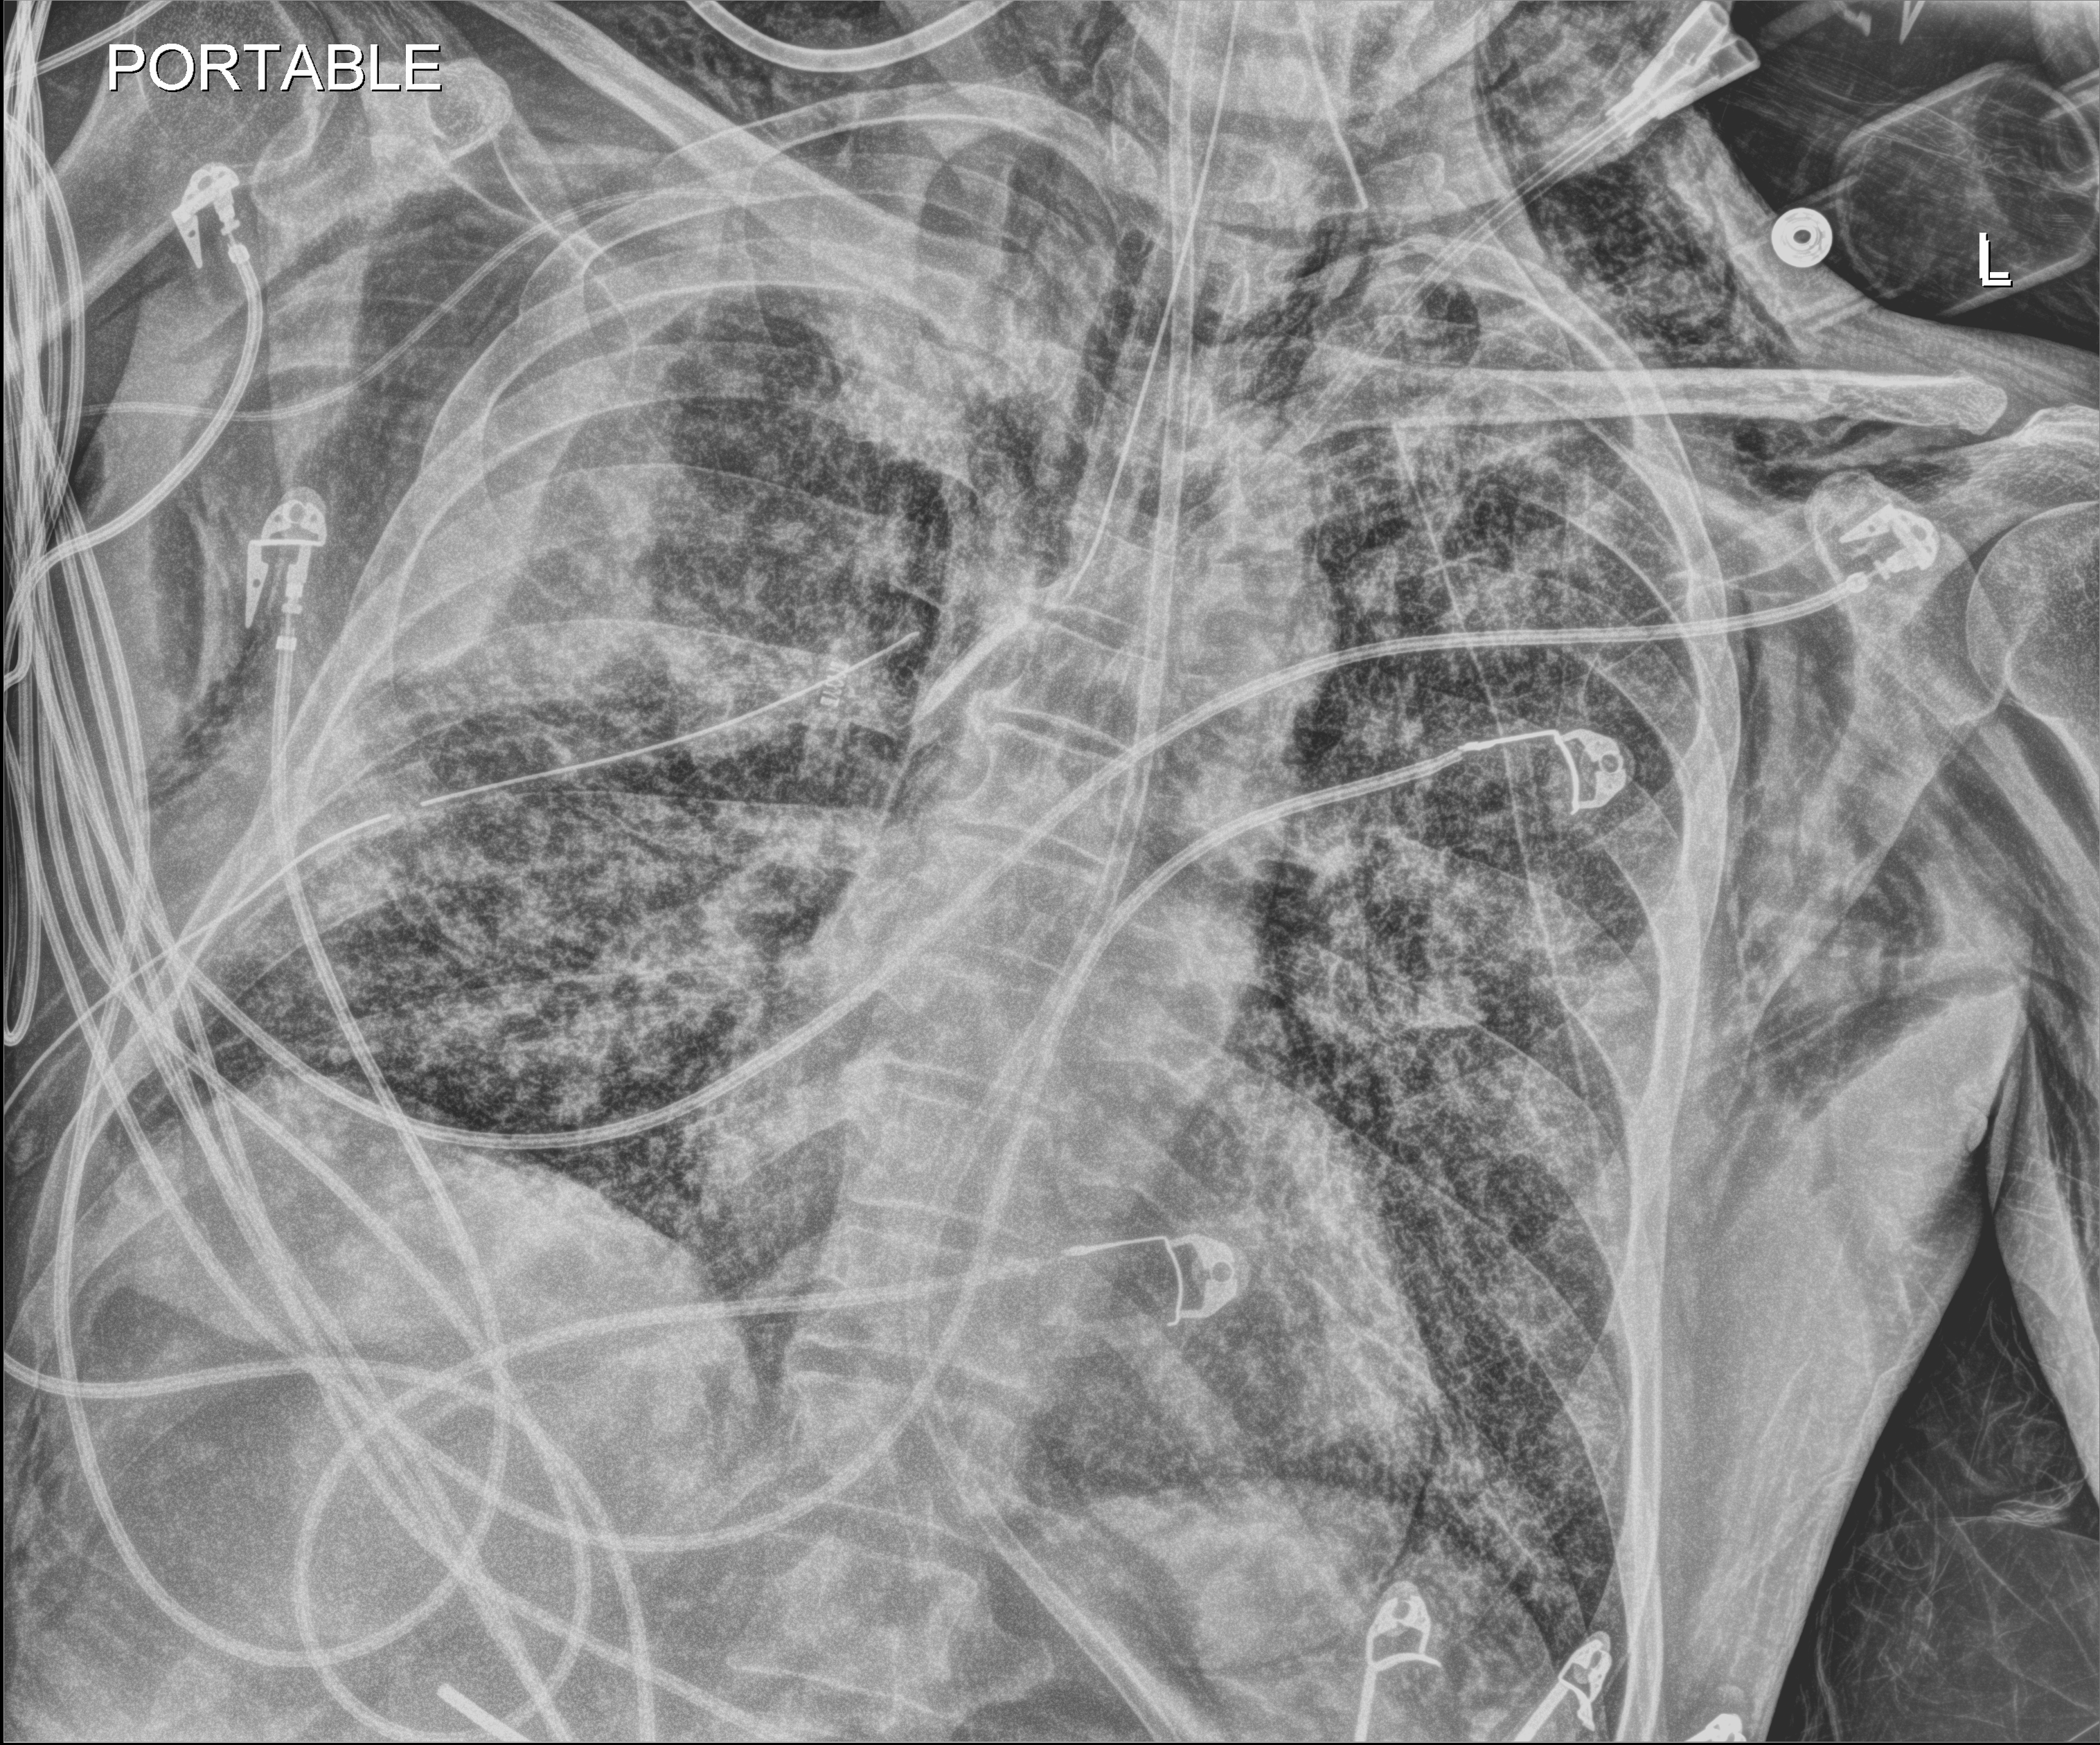
Portable chest radiograph. Patient hospitalised with COVID-19; male, aged 18–59 years.
Admission-level facts for this patient (not findings on this image; timing relative to this image not recorded): diabetes (admission record): no; COPD (admission record): no.